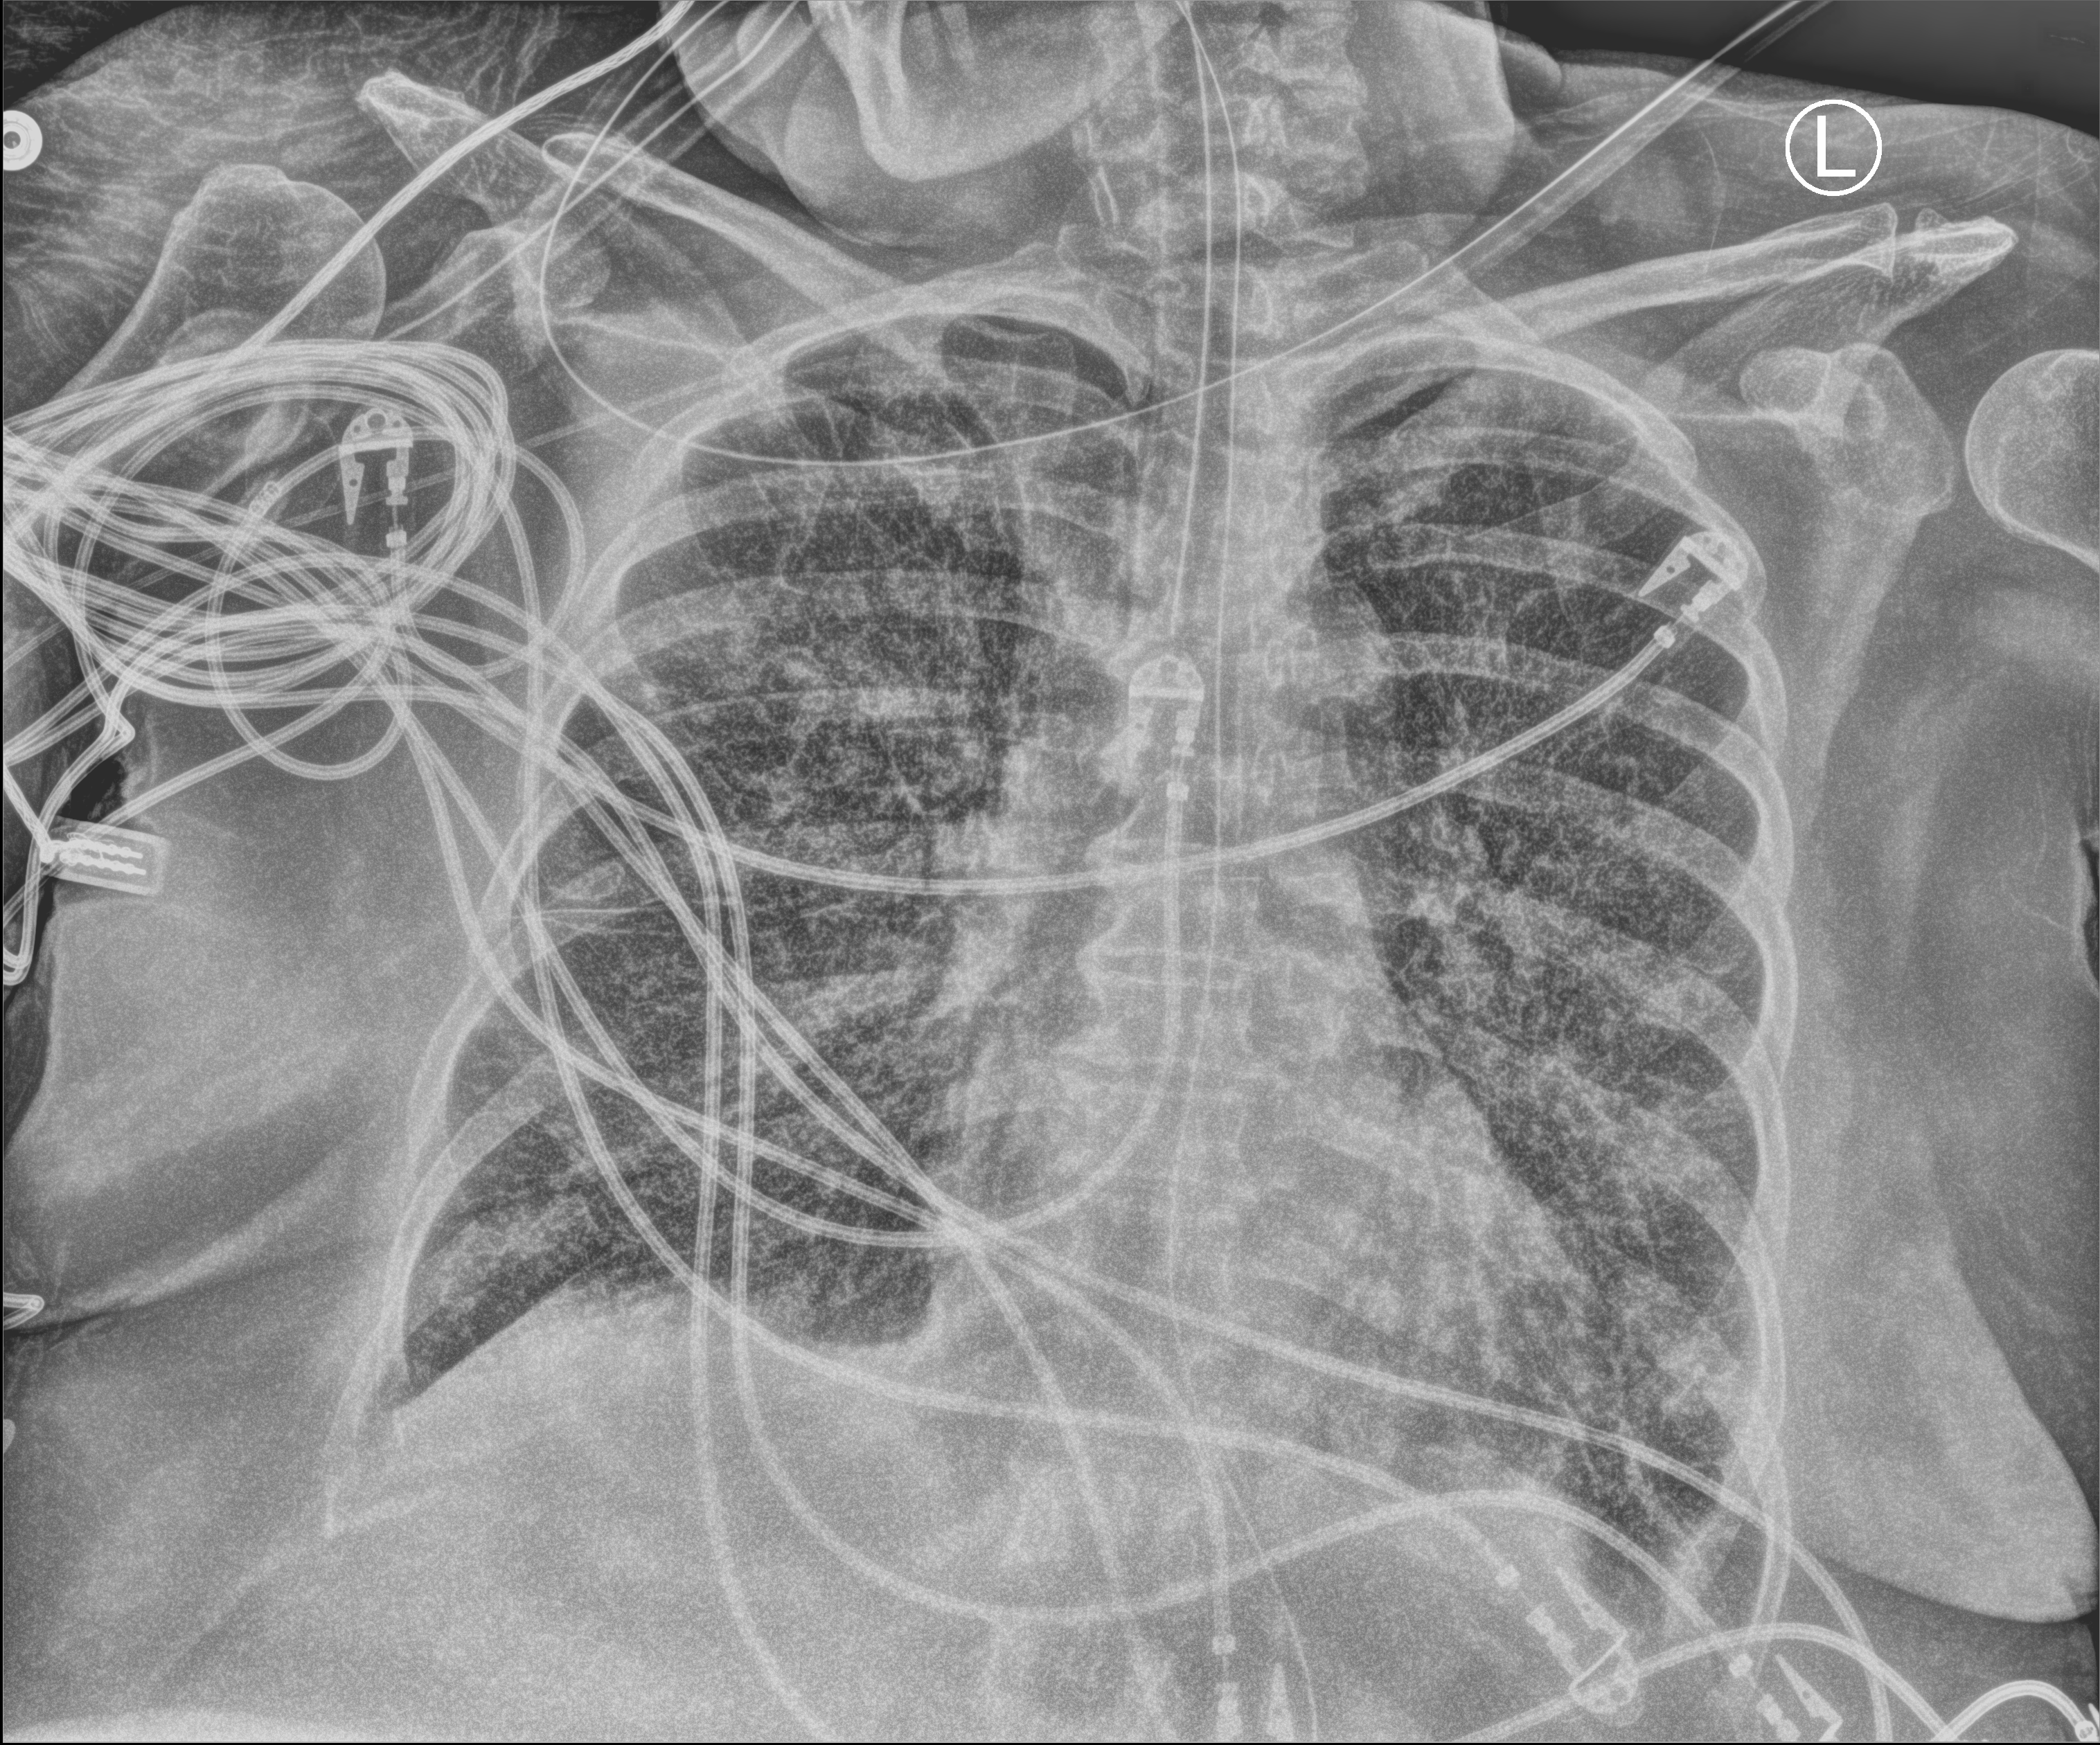
Bedside chest radiograph (computed radiography), anteroposterior (AP) projection. Patient hospitalised with COVID-19; female, aged 60–74 years.
From the hospital-stay record, not from the radiograph (when in the stay this image was taken is not recorded): admitted to intensive care during this hospital stay: yes; mechanically ventilated during this hospital stay: yes; other chronic lung disease (admission record): no.